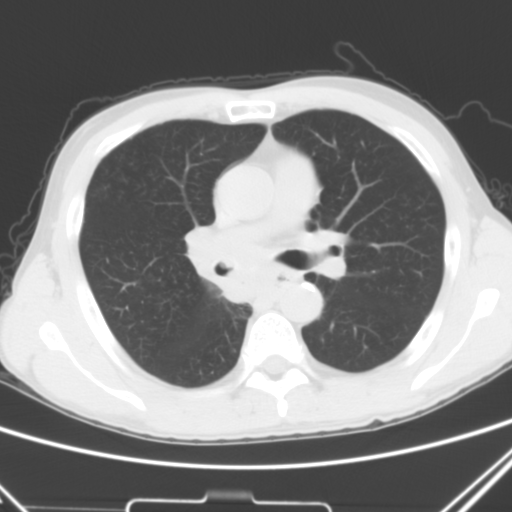
Chest CT, one axial slice. Position 28 of 51 along the scan axis. Lung window (W 1500 / L -600 HU). 512 × 512 image matrix, field of view 327 × 327 mm. Male patient, age 52 years. Case-level facts recorded for this patient, not image findings: clinical TNM (as recorded): T2a N0 M1c.
Structures marked on this image (bounding box drawn by a radiologist):
- lung tumour (recorded histology: squamous cell carcinoma): box from (x=180, y=221) to (x=250, y=318) px